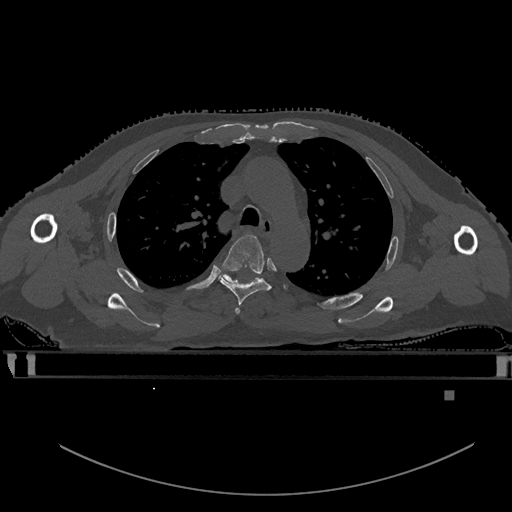
CT including the spine, one axial slice; position 401 of 969 along the scan axis; bone window (W 1800 / L 400 HU); 512 × 512 image matrix, field of view 456 × 456 mm. Male patient, age 82 years. From the clinical record (not read from this slice): primary cancer: prostate.
Annotated regions visible in this slice (semi-automatically segmented with operator editing):
- T3 vertebra: bounding box [x1, y1, x2, y2] px = [235, 308, 240, 314]
- T4 vertebra: [219, 234, 271, 308]
- T5 vertebra: [216, 271, 260, 284]